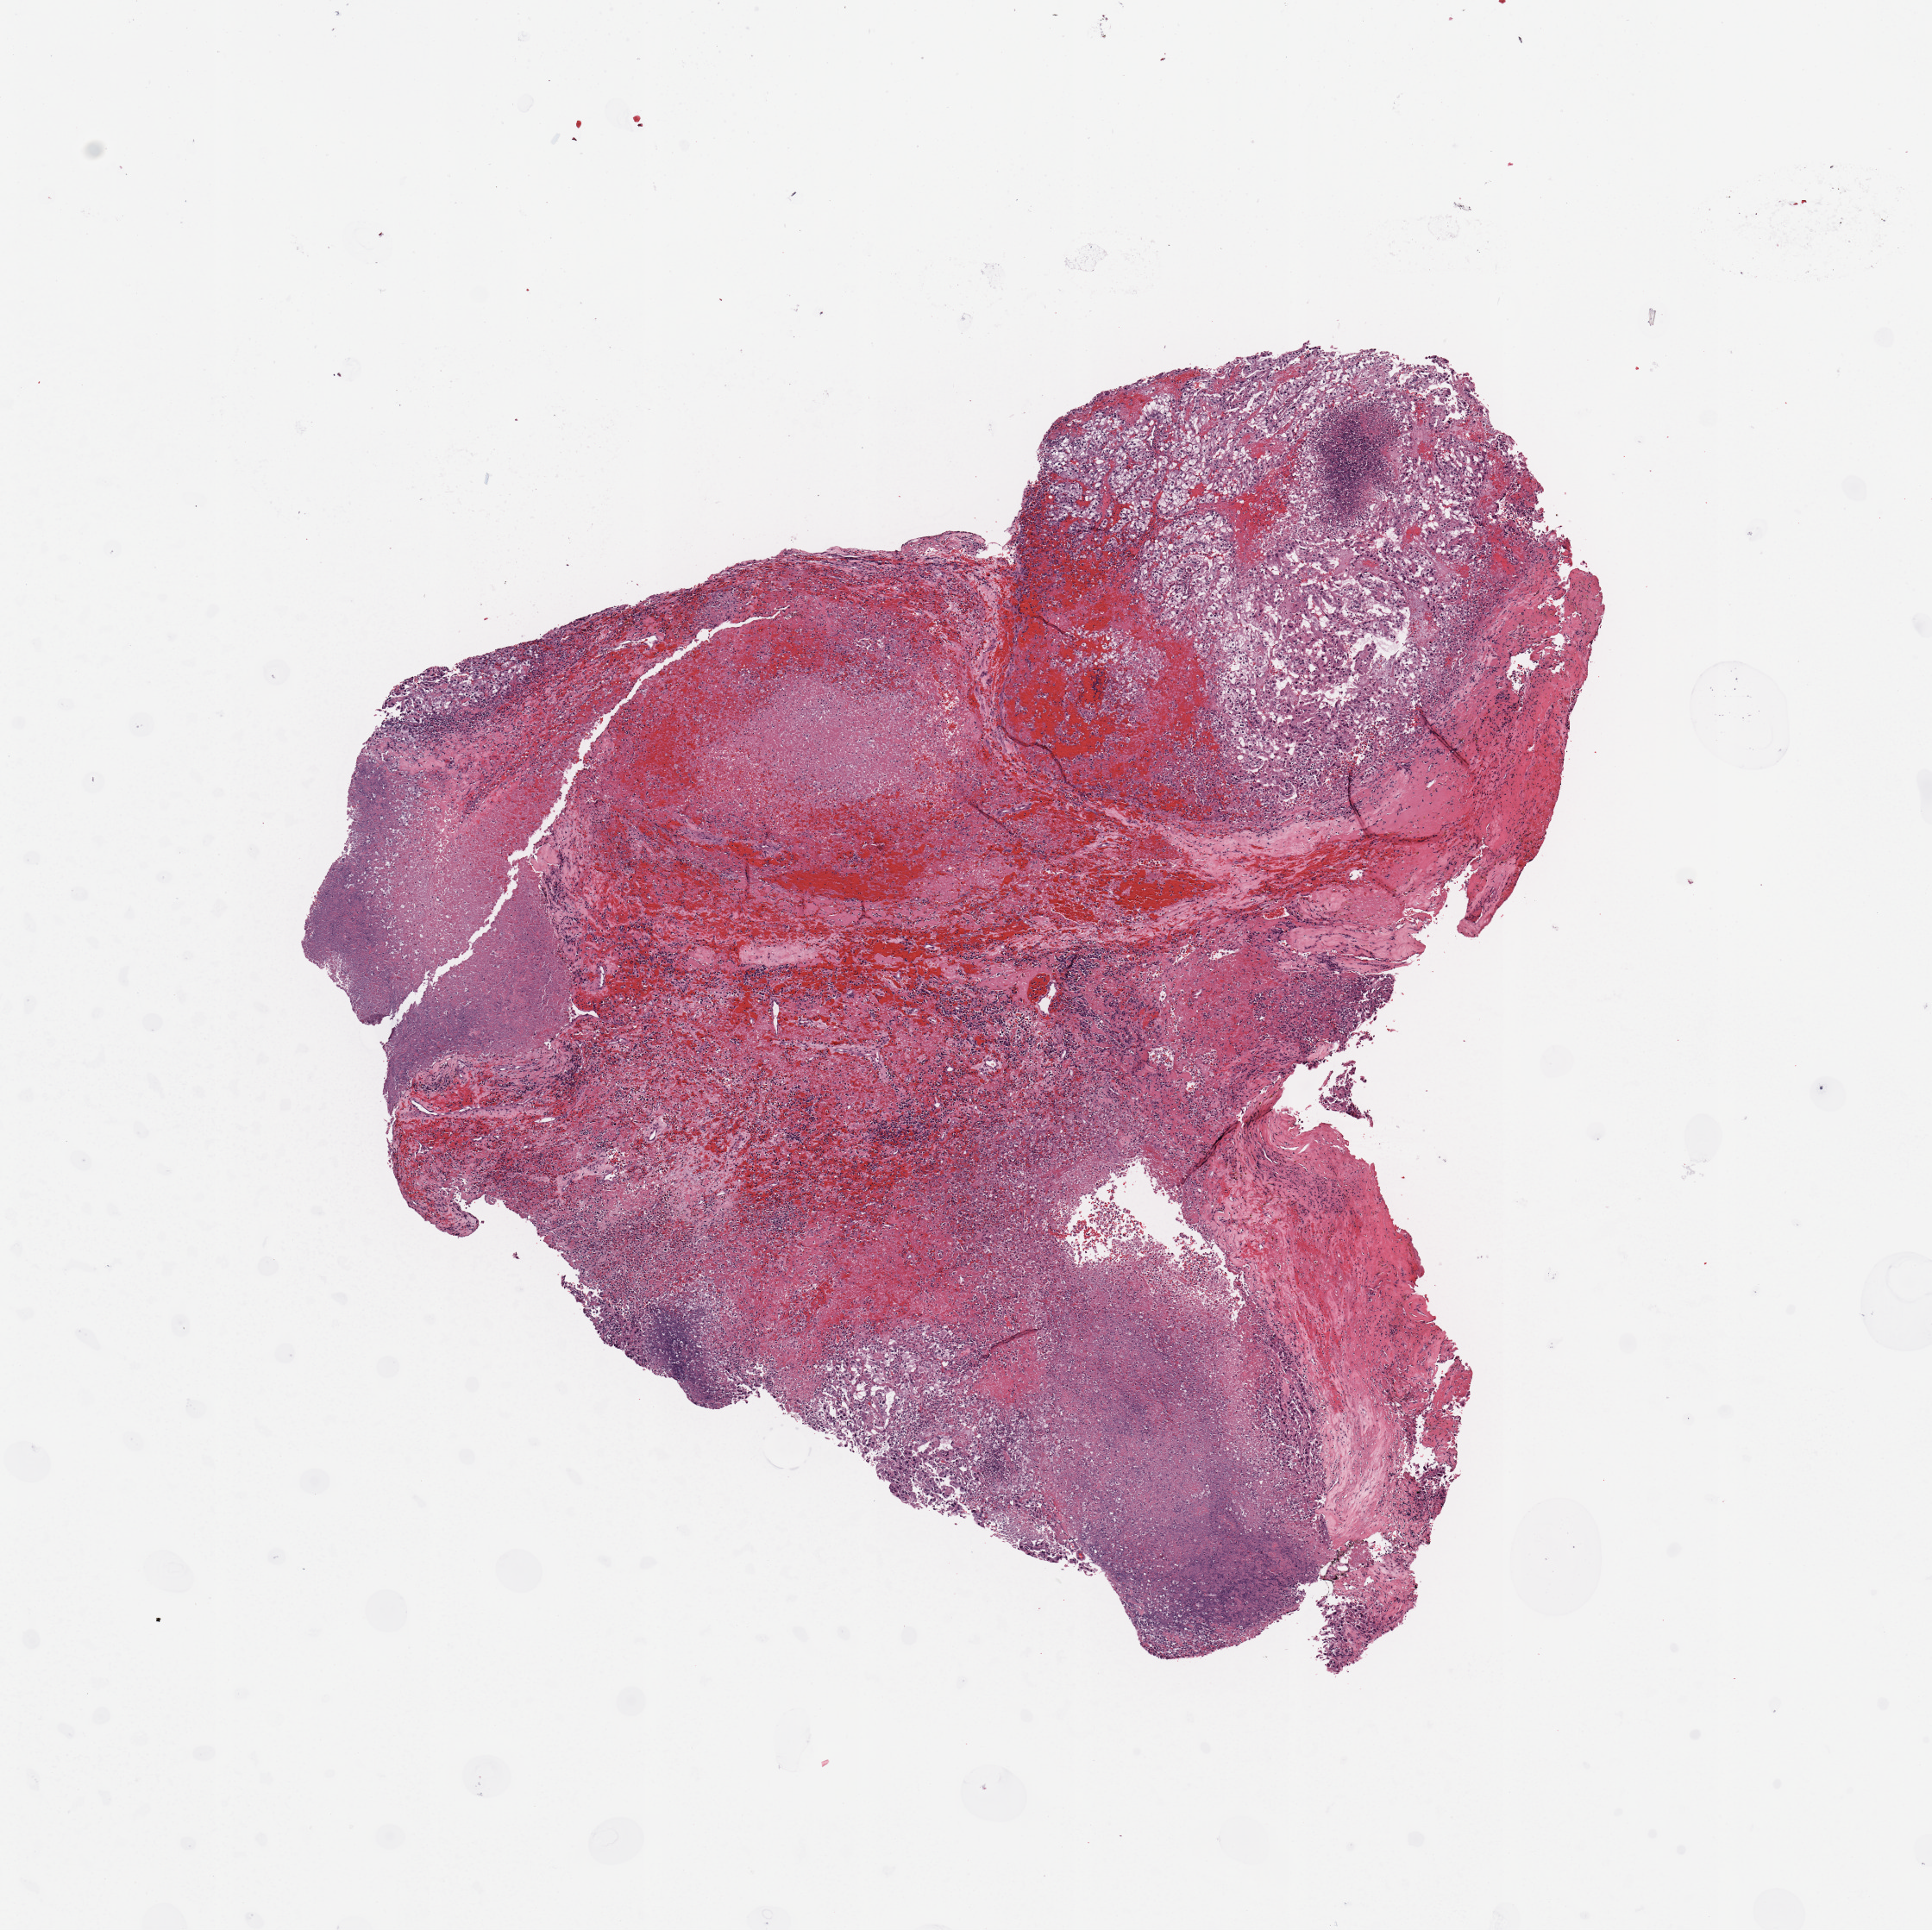
Whole-slide histology image, H&E, shown as a low-resolution overview of the whole scanned area (about 8.9 x 8.9 mm, acquisition: 20x scan). Tumour tissue sample, kidney. Male, 53 y/o. Histologic grade: G3 (poorly differentiated).
Primary tumour site (as recorded): middle. Diagnosis: Renal cell carcinoma, NOS. AJCC pathologic stage: II.